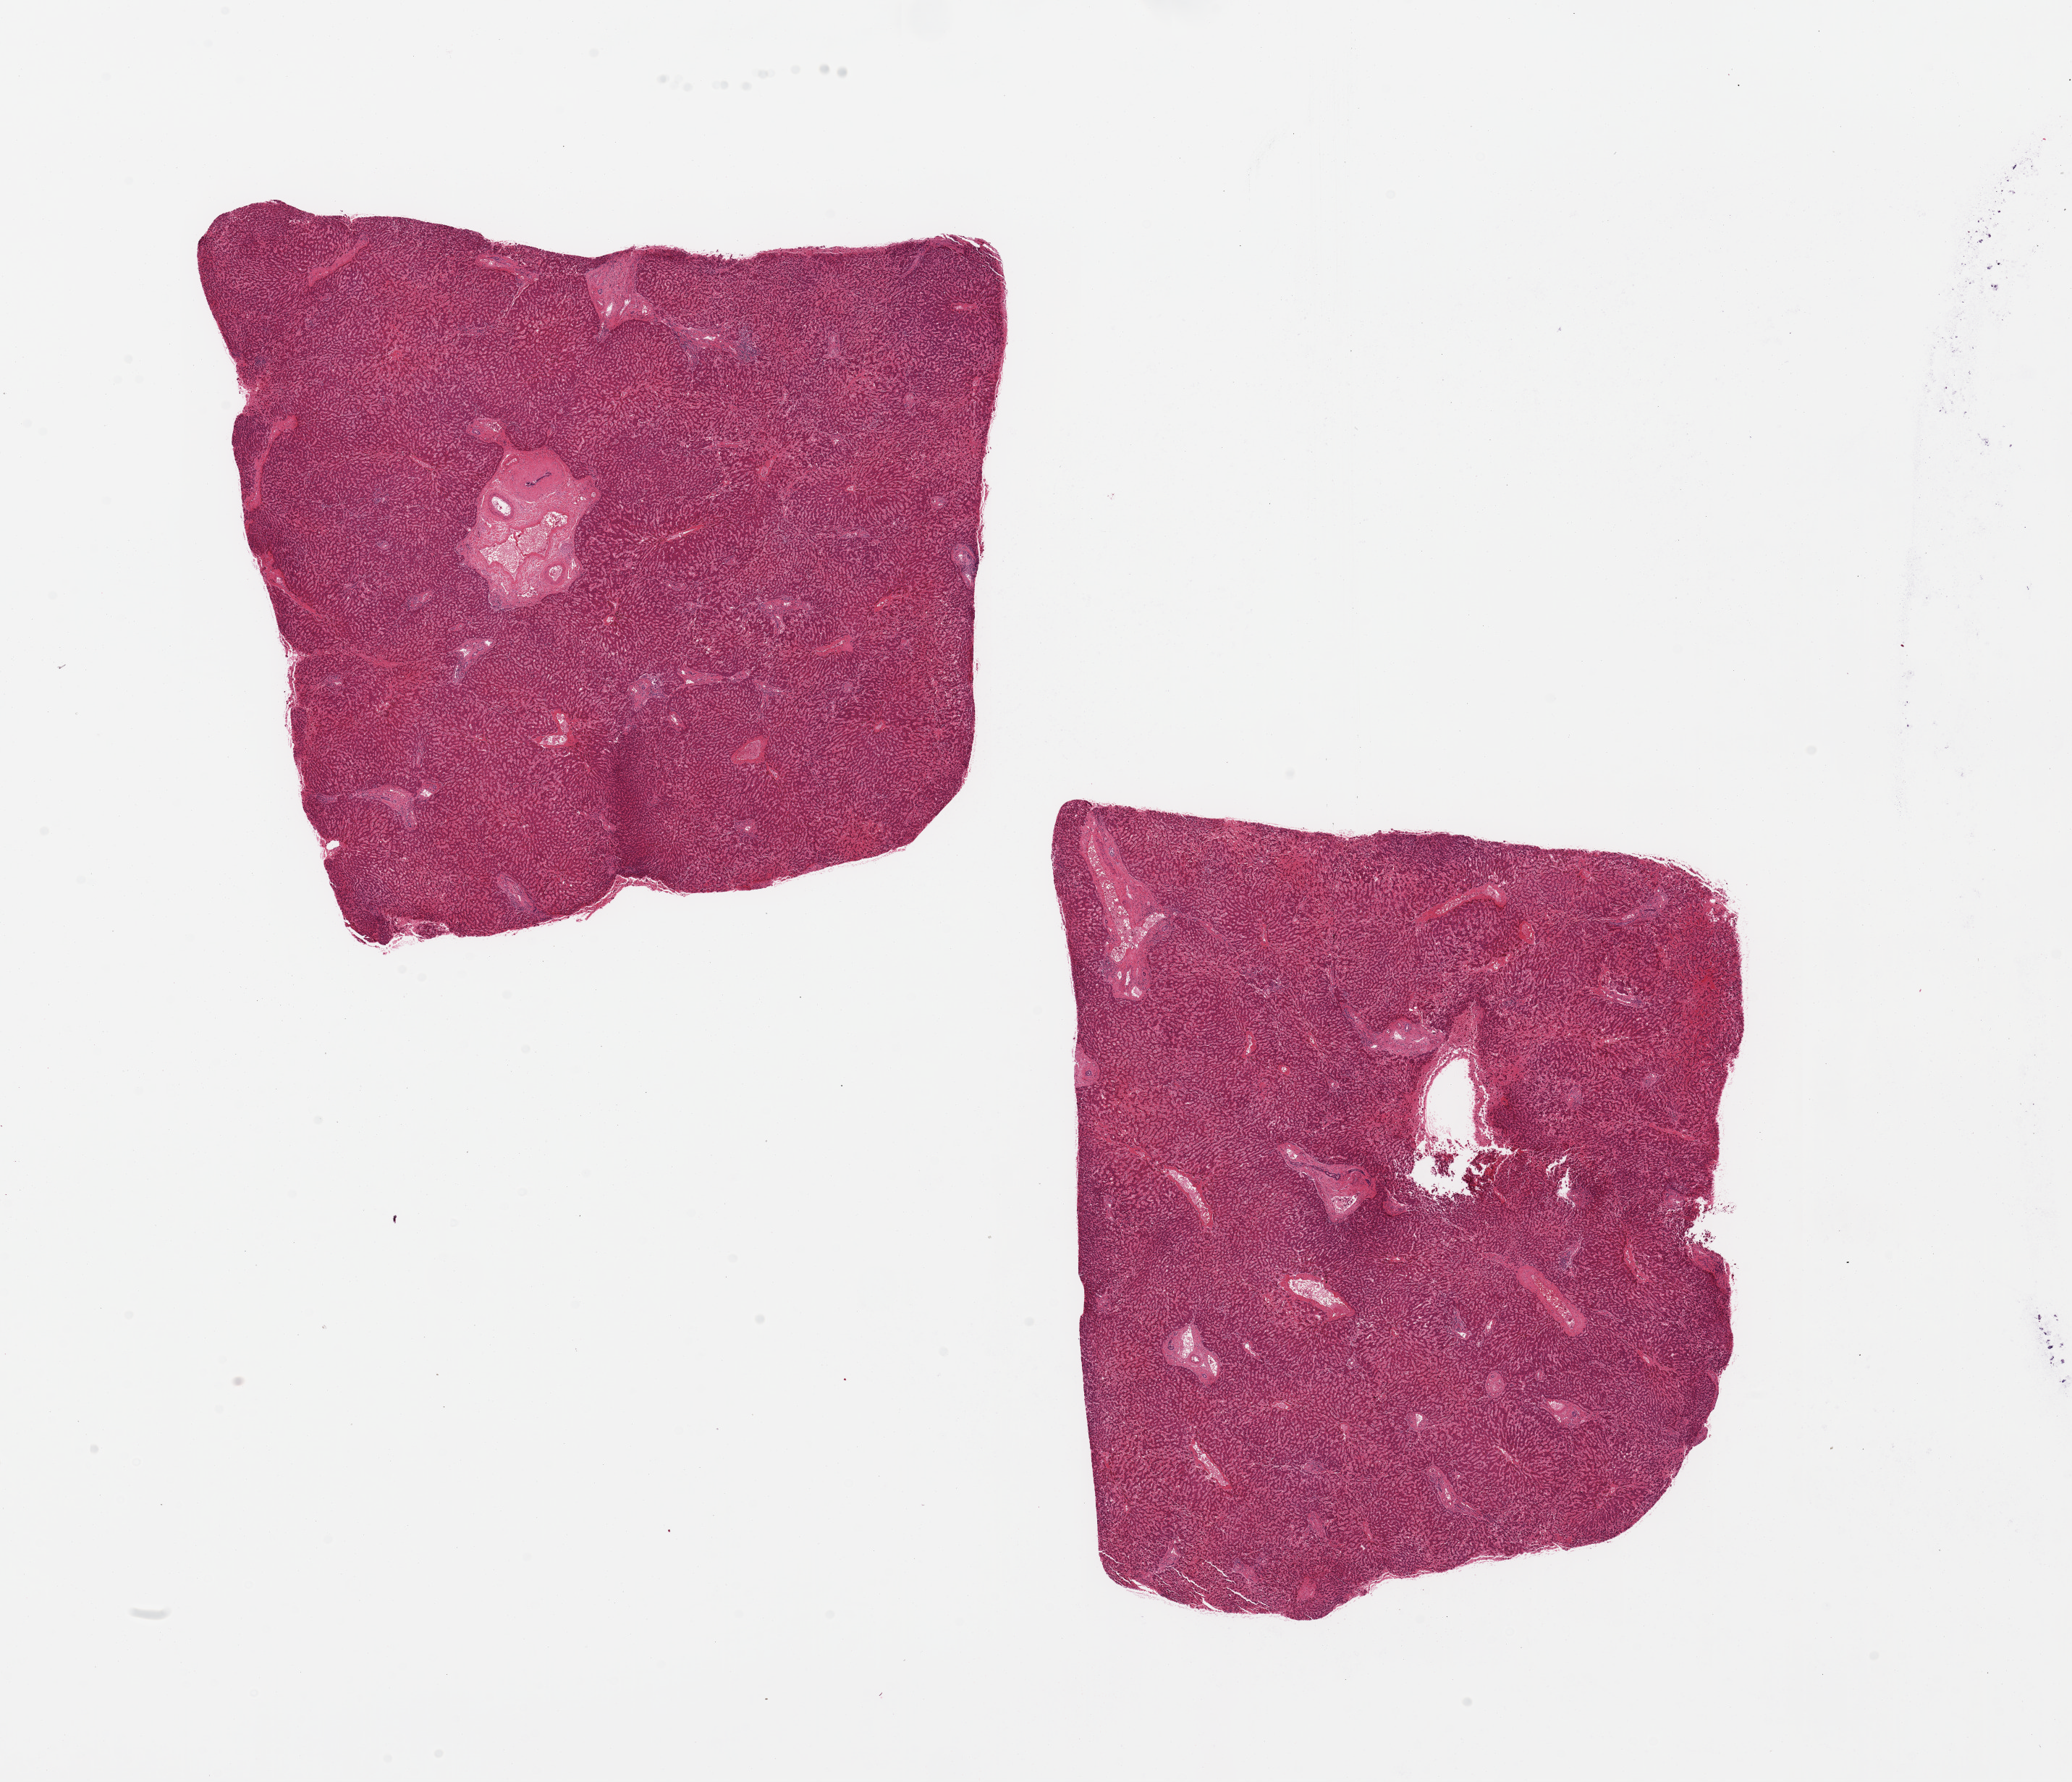
Whole-slide image, H&E stain — whole scanned area (about 22.6 x 19.5 mm, slide scanned at 20x) shown as a low-resolution overview; PAXgene-fixed, paraffin-embedded tissue; sampled site (target tissue): liver; tissue donor sample.
• pathologist's review note for this sample: 2 pieces, moderate passive congestion